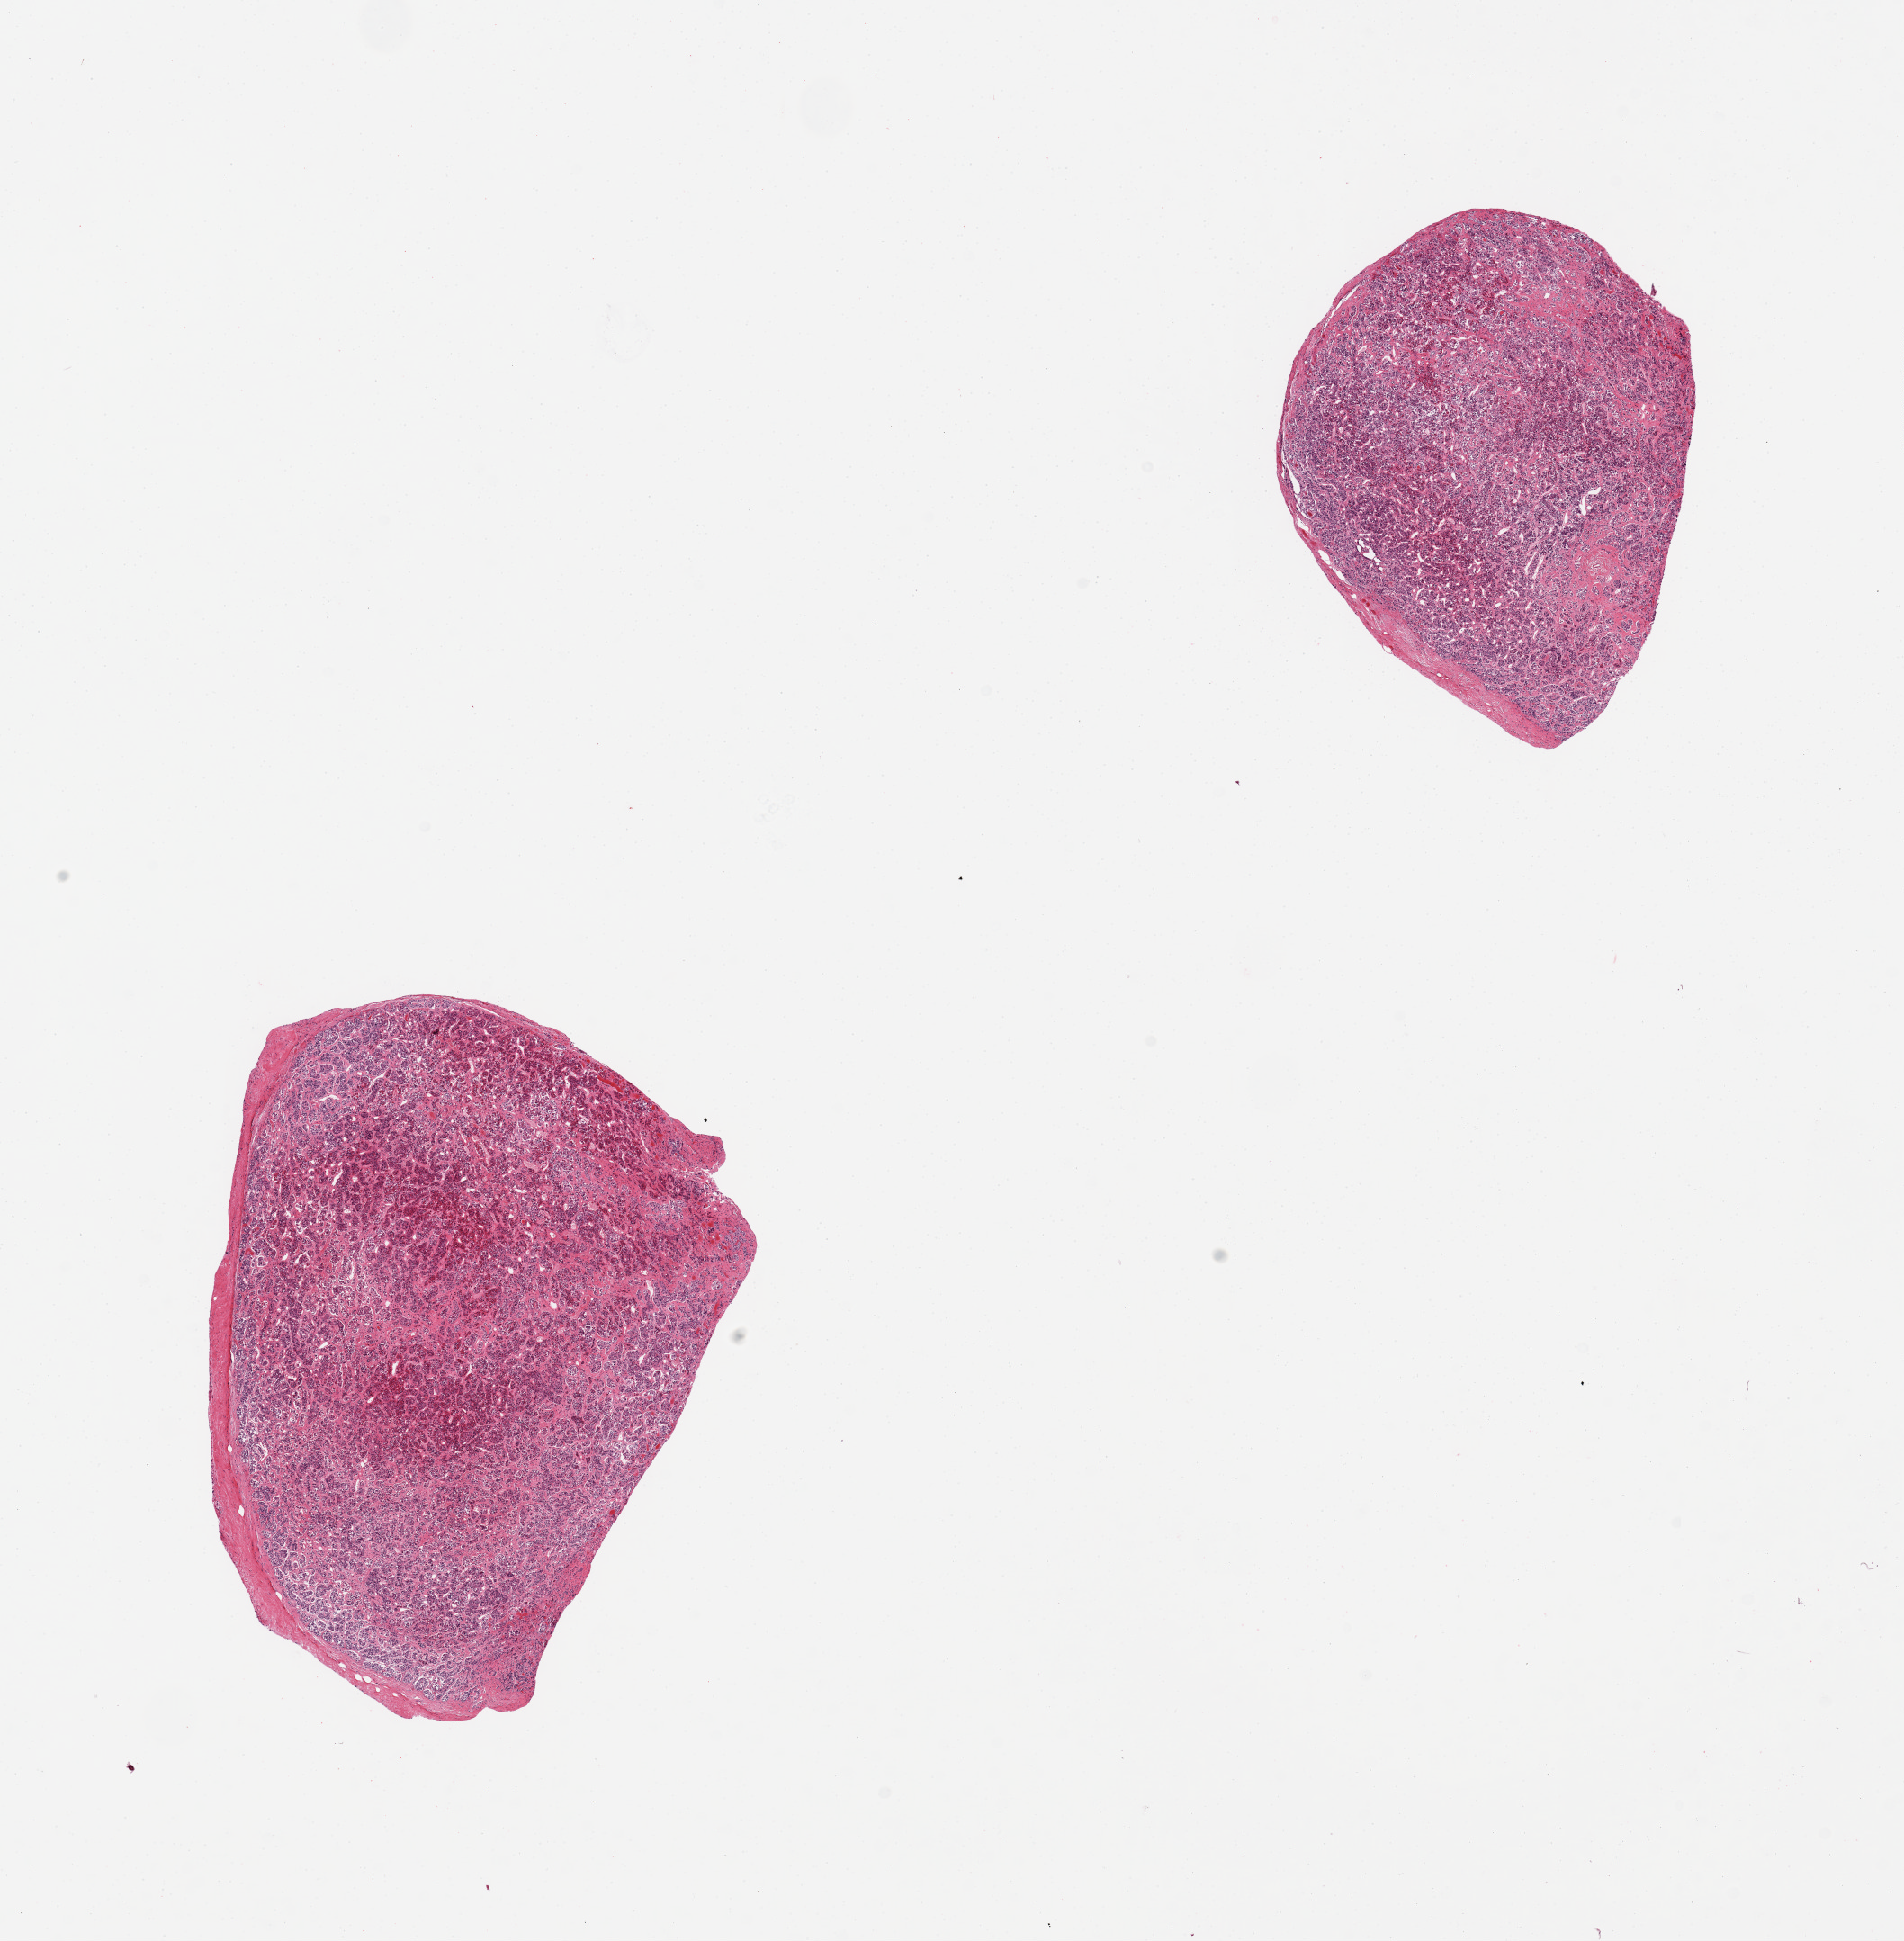
H&E whole-slide image, brightfield, shown as a low-resolution overview of the whole scanned area (about 16.7 x 17.1 mm, from a 20x scan), PAXgene-fixed paraffin-embedded (PFPE) section, target tissue: pituitary, donor tissue sample.
Reviewer comment on this tissue sample: 2 pieces, adenophypophysis.